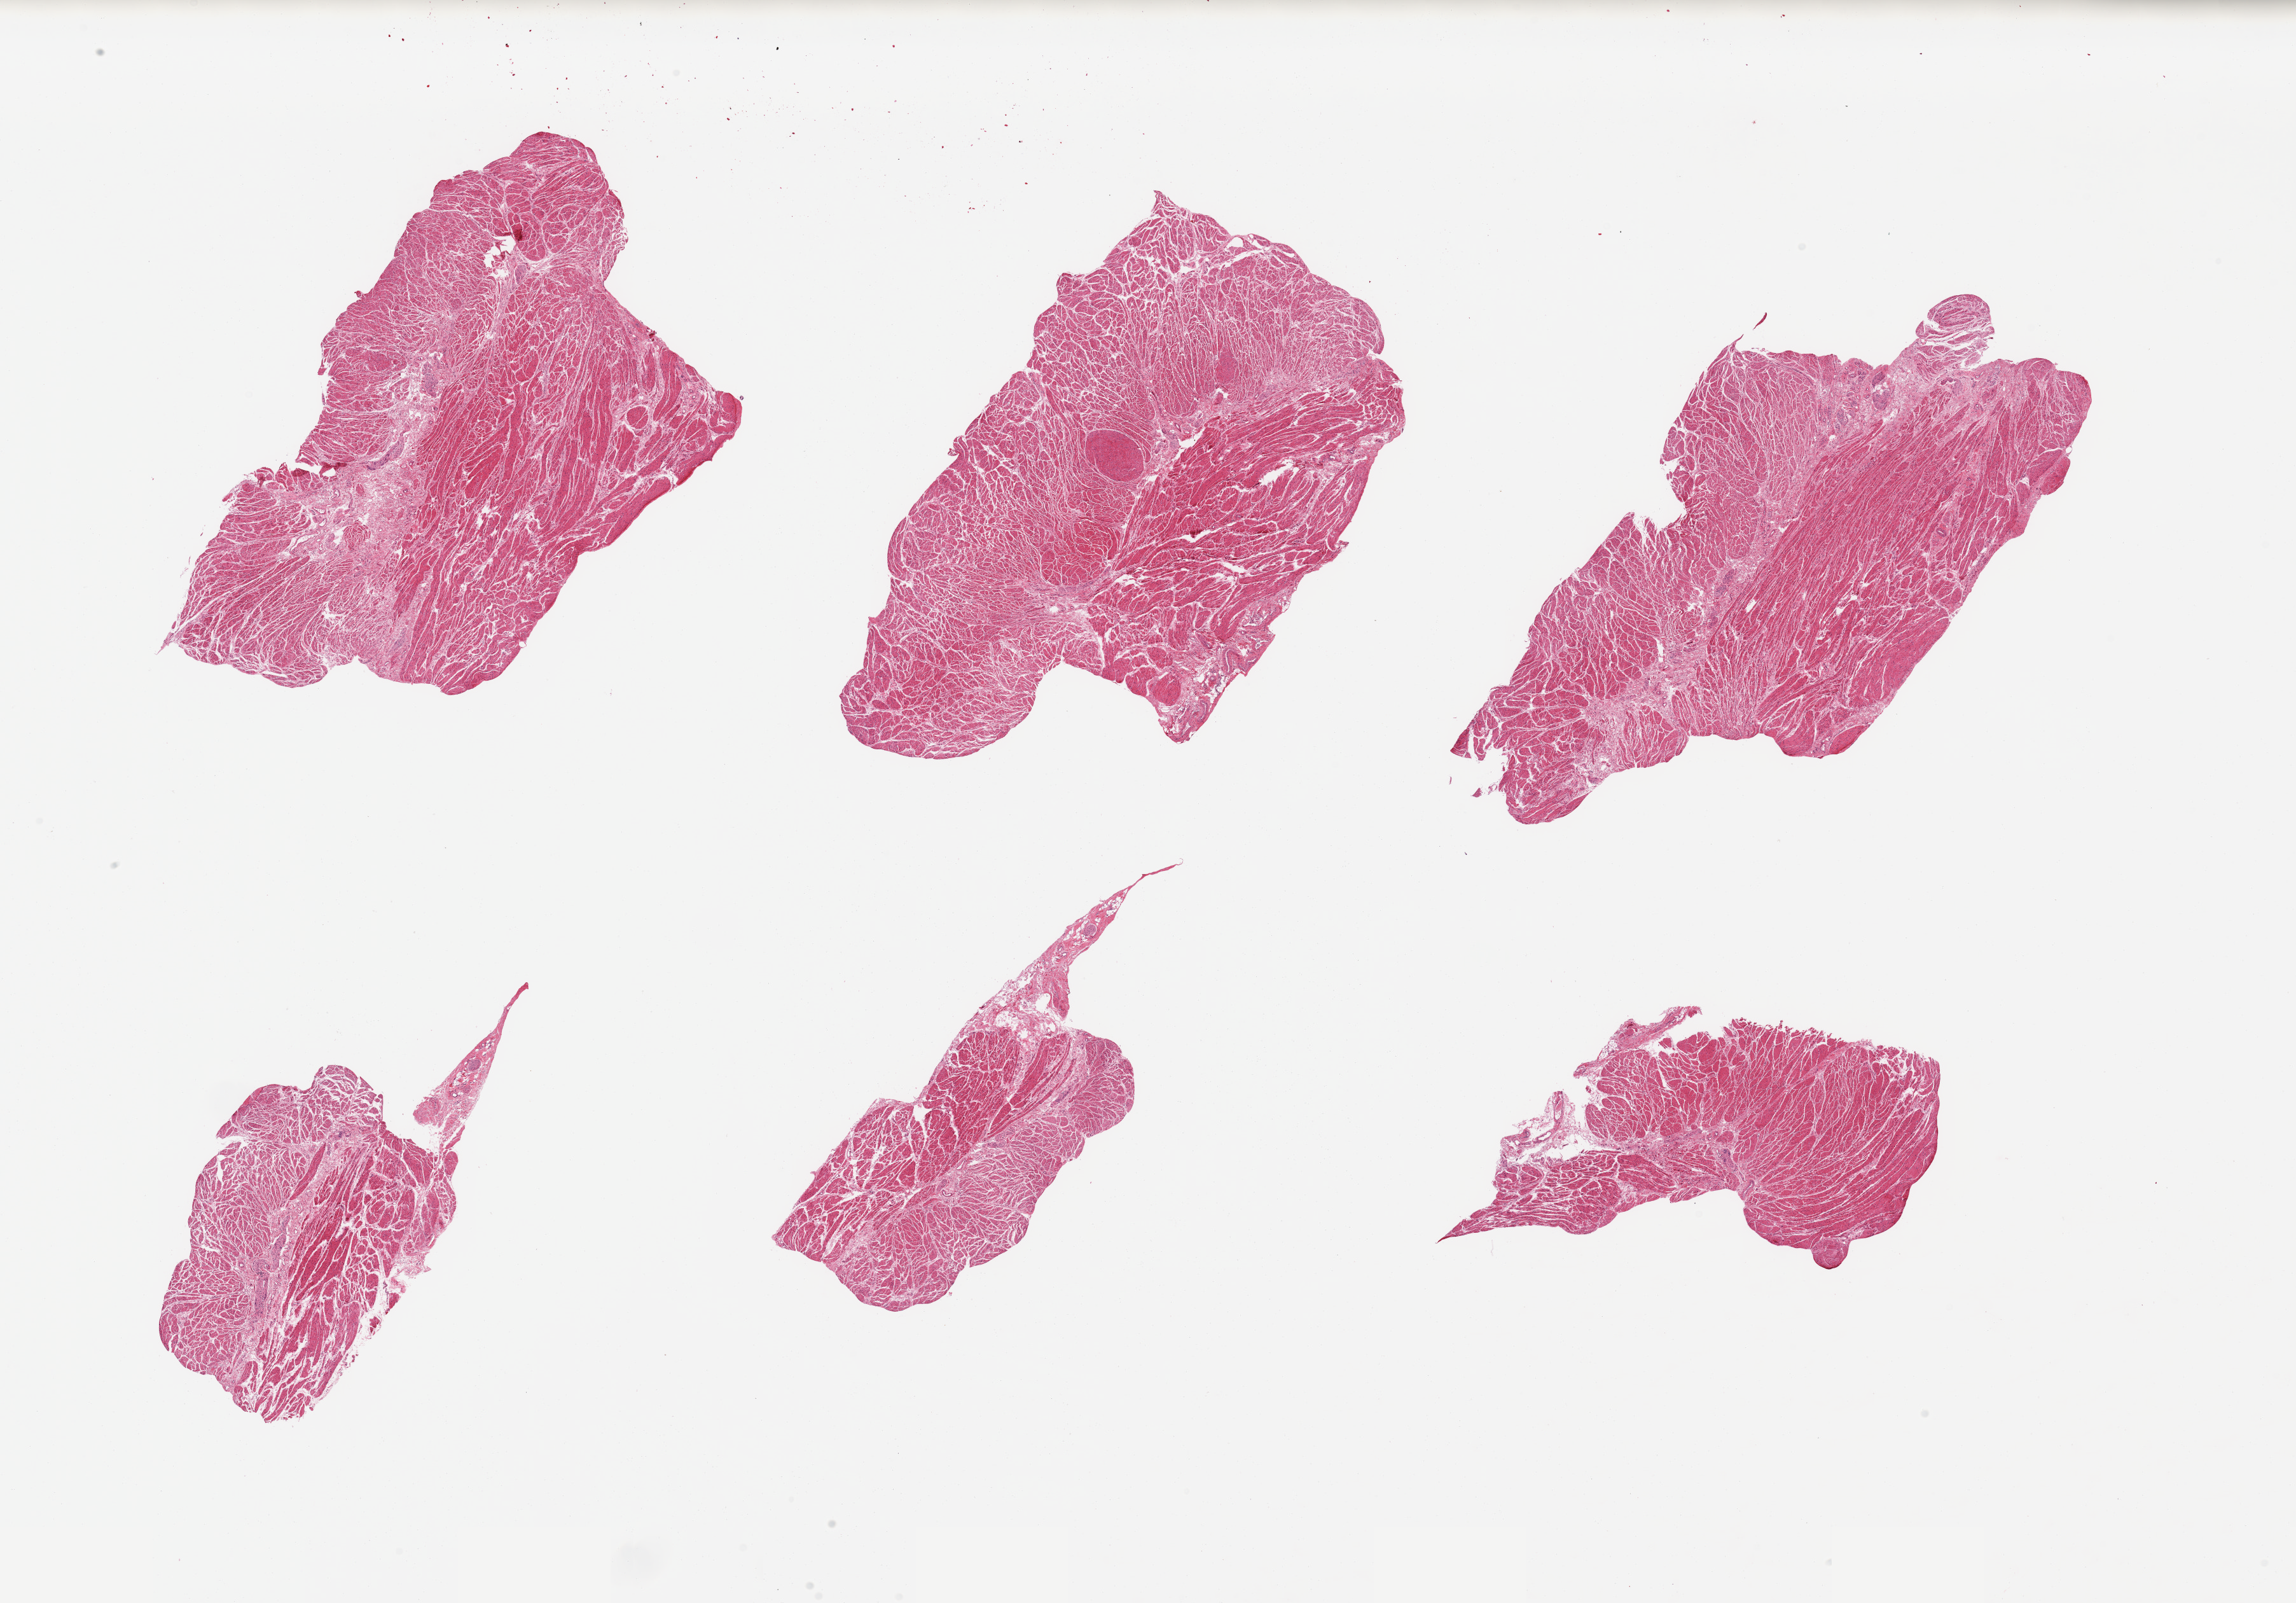
Haematoxylin and eosin whole-slide image, brightfield, shown as a low-resolution overview of the whole scanned area (about 28.5 x 19.9 mm, from a 20x scan); PAXgene-fixed, paraffin-embedded tissue; target tissue: gastroesophageal junction; tissue donor sample.
Pathologist's review note for this sample: 6 pieces, confirmed target muscularis.